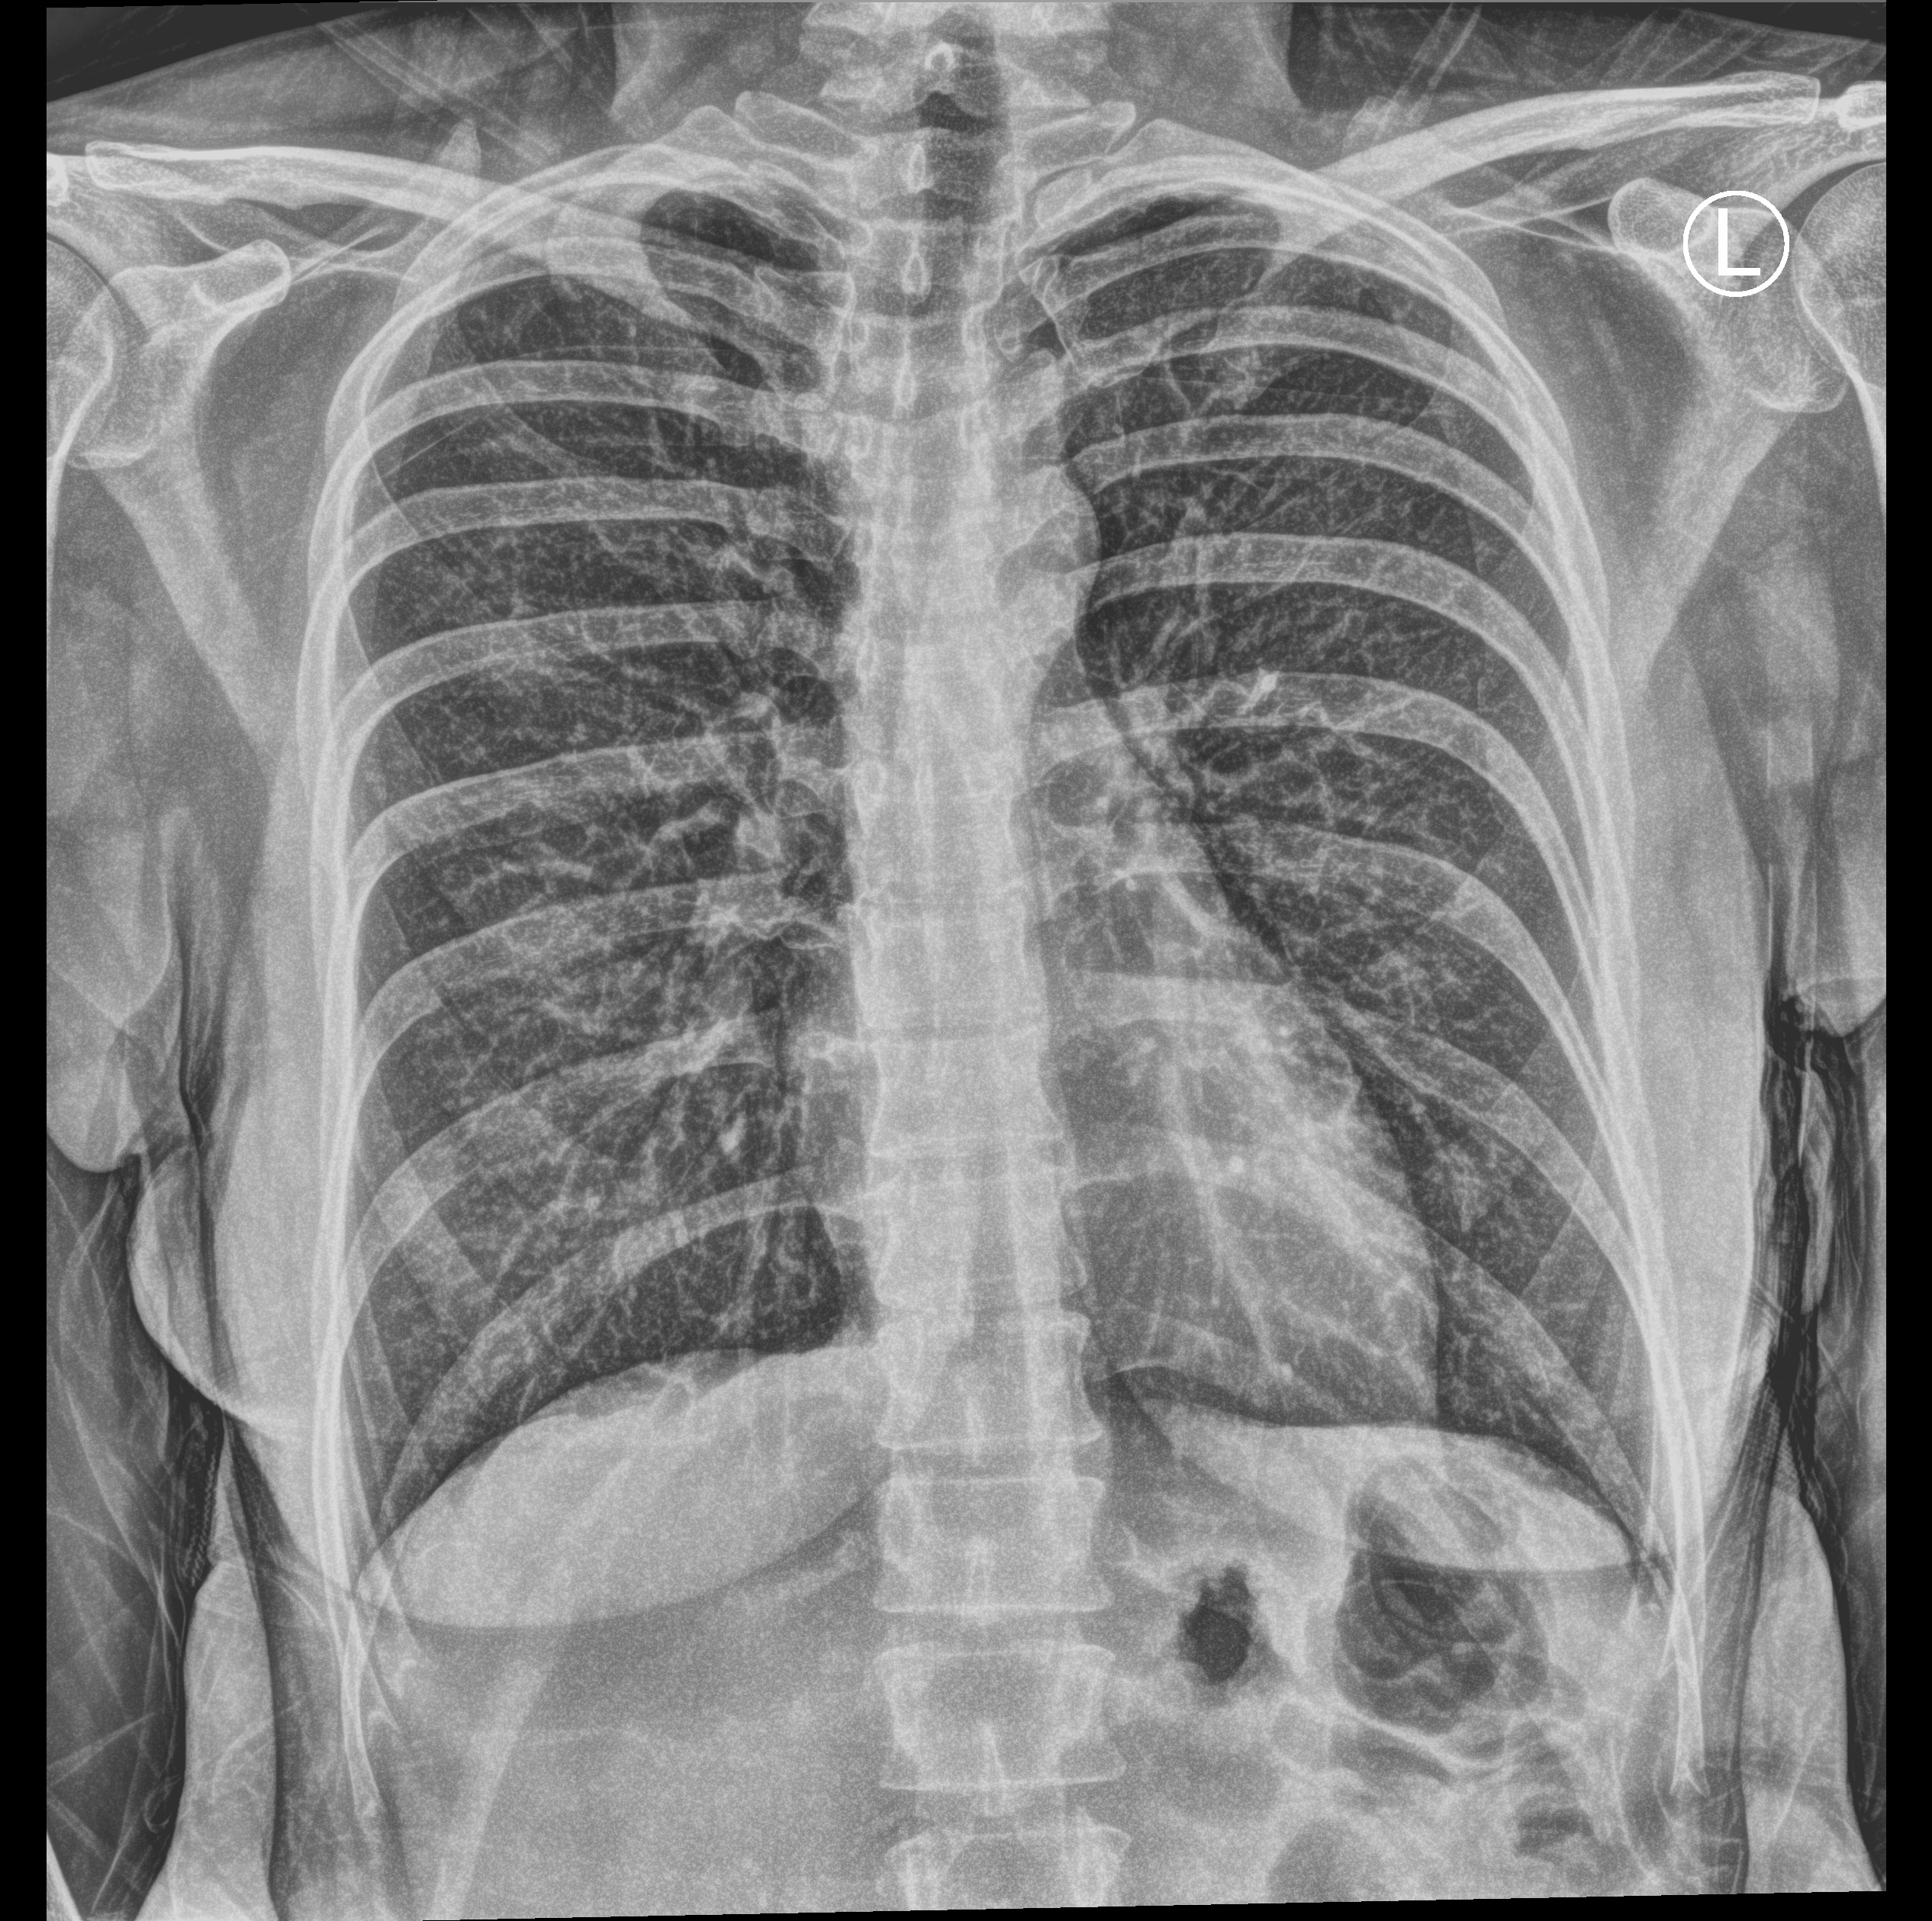
Portable chest radiograph. Female patient hospitalised with COVID-19, age 18–59 years.
Admission-level facts for this patient (not findings on this image; timing relative to this image not recorded):
- mechanically ventilated during this hospital stay: no
- admitted to intensive care during this hospital stay: no